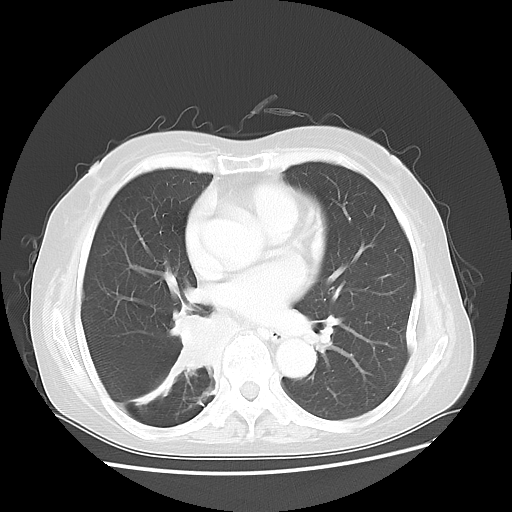
Chest CT, one axial slice; position 22 of 47 along the scan axis; 120 kVp; lung window (W 1500 / L -600 HU); 5 mm slice thickness; 512 × 512 image matrix, field of view 360 × 360 mm. Female patient, age 63 years. Case-level facts recorded for this patient, not image findings: clinical TNM (as recorded): T2 N3 M1b; histopathological grade: G3.
Annotated regions visible in this slice (bounding box drawn by a radiologist):
- lung tumour (recorded histology: small cell carcinoma): box from (x=159, y=302) to (x=229, y=377) px